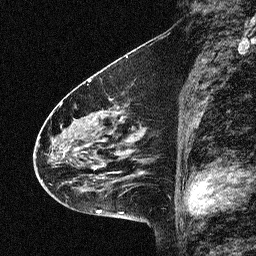
Breast MRI (dynamic contrast-enhanced), one sagittal slice. Dynamic contrast-enhanced study with each time point stored as its own series, time point 2 of 3 at this slice position (early post-contrast, ordered by acquisition time). 1.5 T. TE 4.5 ms, TR 11 ms. 2.06 mm slice thickness. 256 × 256 image matrix, field of view 200 × 200 mm. Female patient, age 46 years. Case-level facts recorded for this patient, not image findings: setting: breast cancer imaged before/during neoadjuvant chemotherapy; receptor status: HER2-positive.
Outlined on this slice (semi-automatically segmented with operator editing):
- analysis volume of interest (the breast-tissue region the enhancement analysis was run in; not a lesion): bounding box (x1, y1, x2, y2) in pixels: (42, 80, 150, 180)
- tumour enhancement mask (voxels above the 90 % enhancement threshold inside the analysis volume of interest): (74, 104, 142, 180)